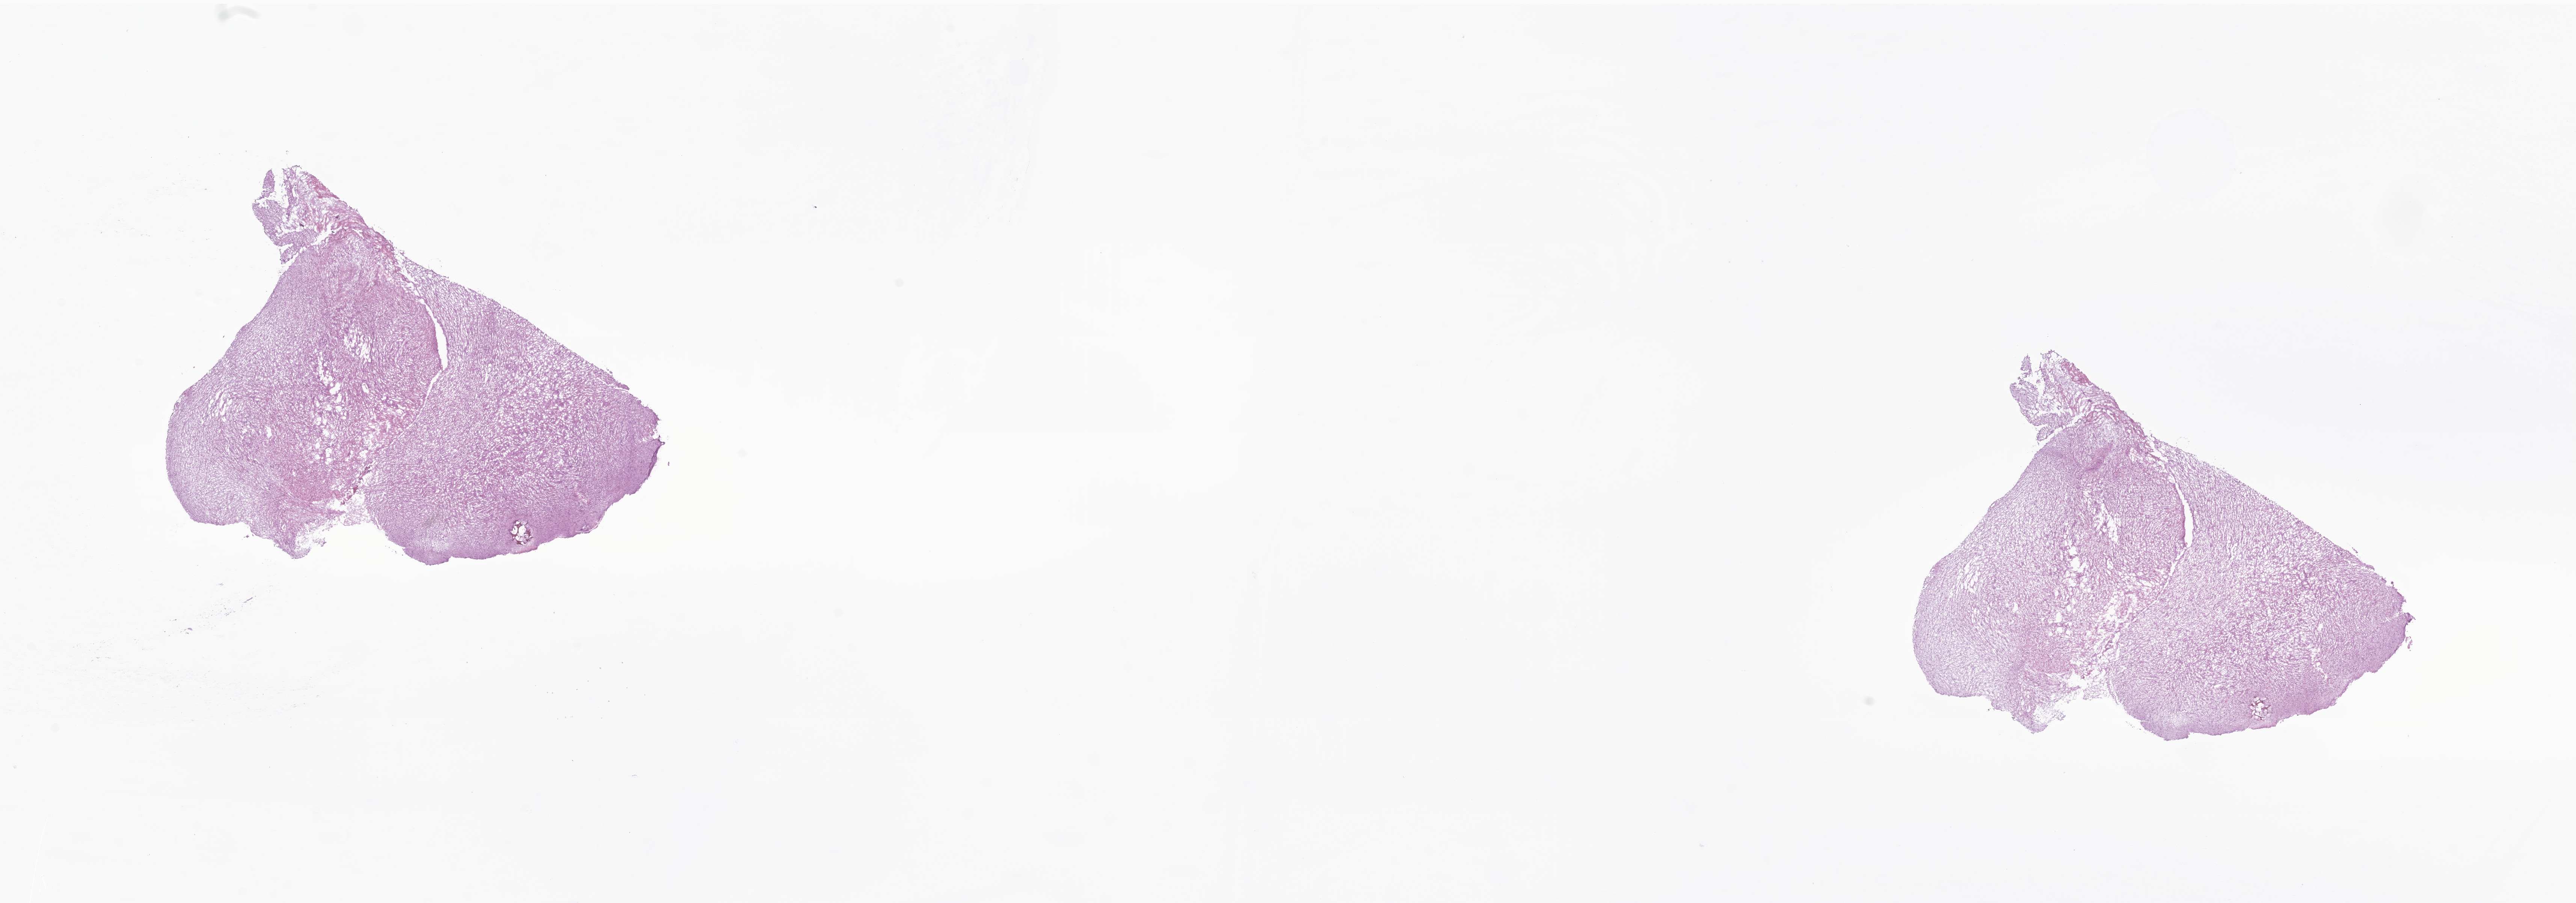
Whole-slide image, H&E stain of tumor tissue from the brain — low-resolution overview of the scanned area, about 28.9 x 10.1 mm. Frozen section (OCT-embedded). Patient male; age 217 months (18 years 1 month).
Diagnosis (ICD-O-3 morphology term): Glioma, malignant.